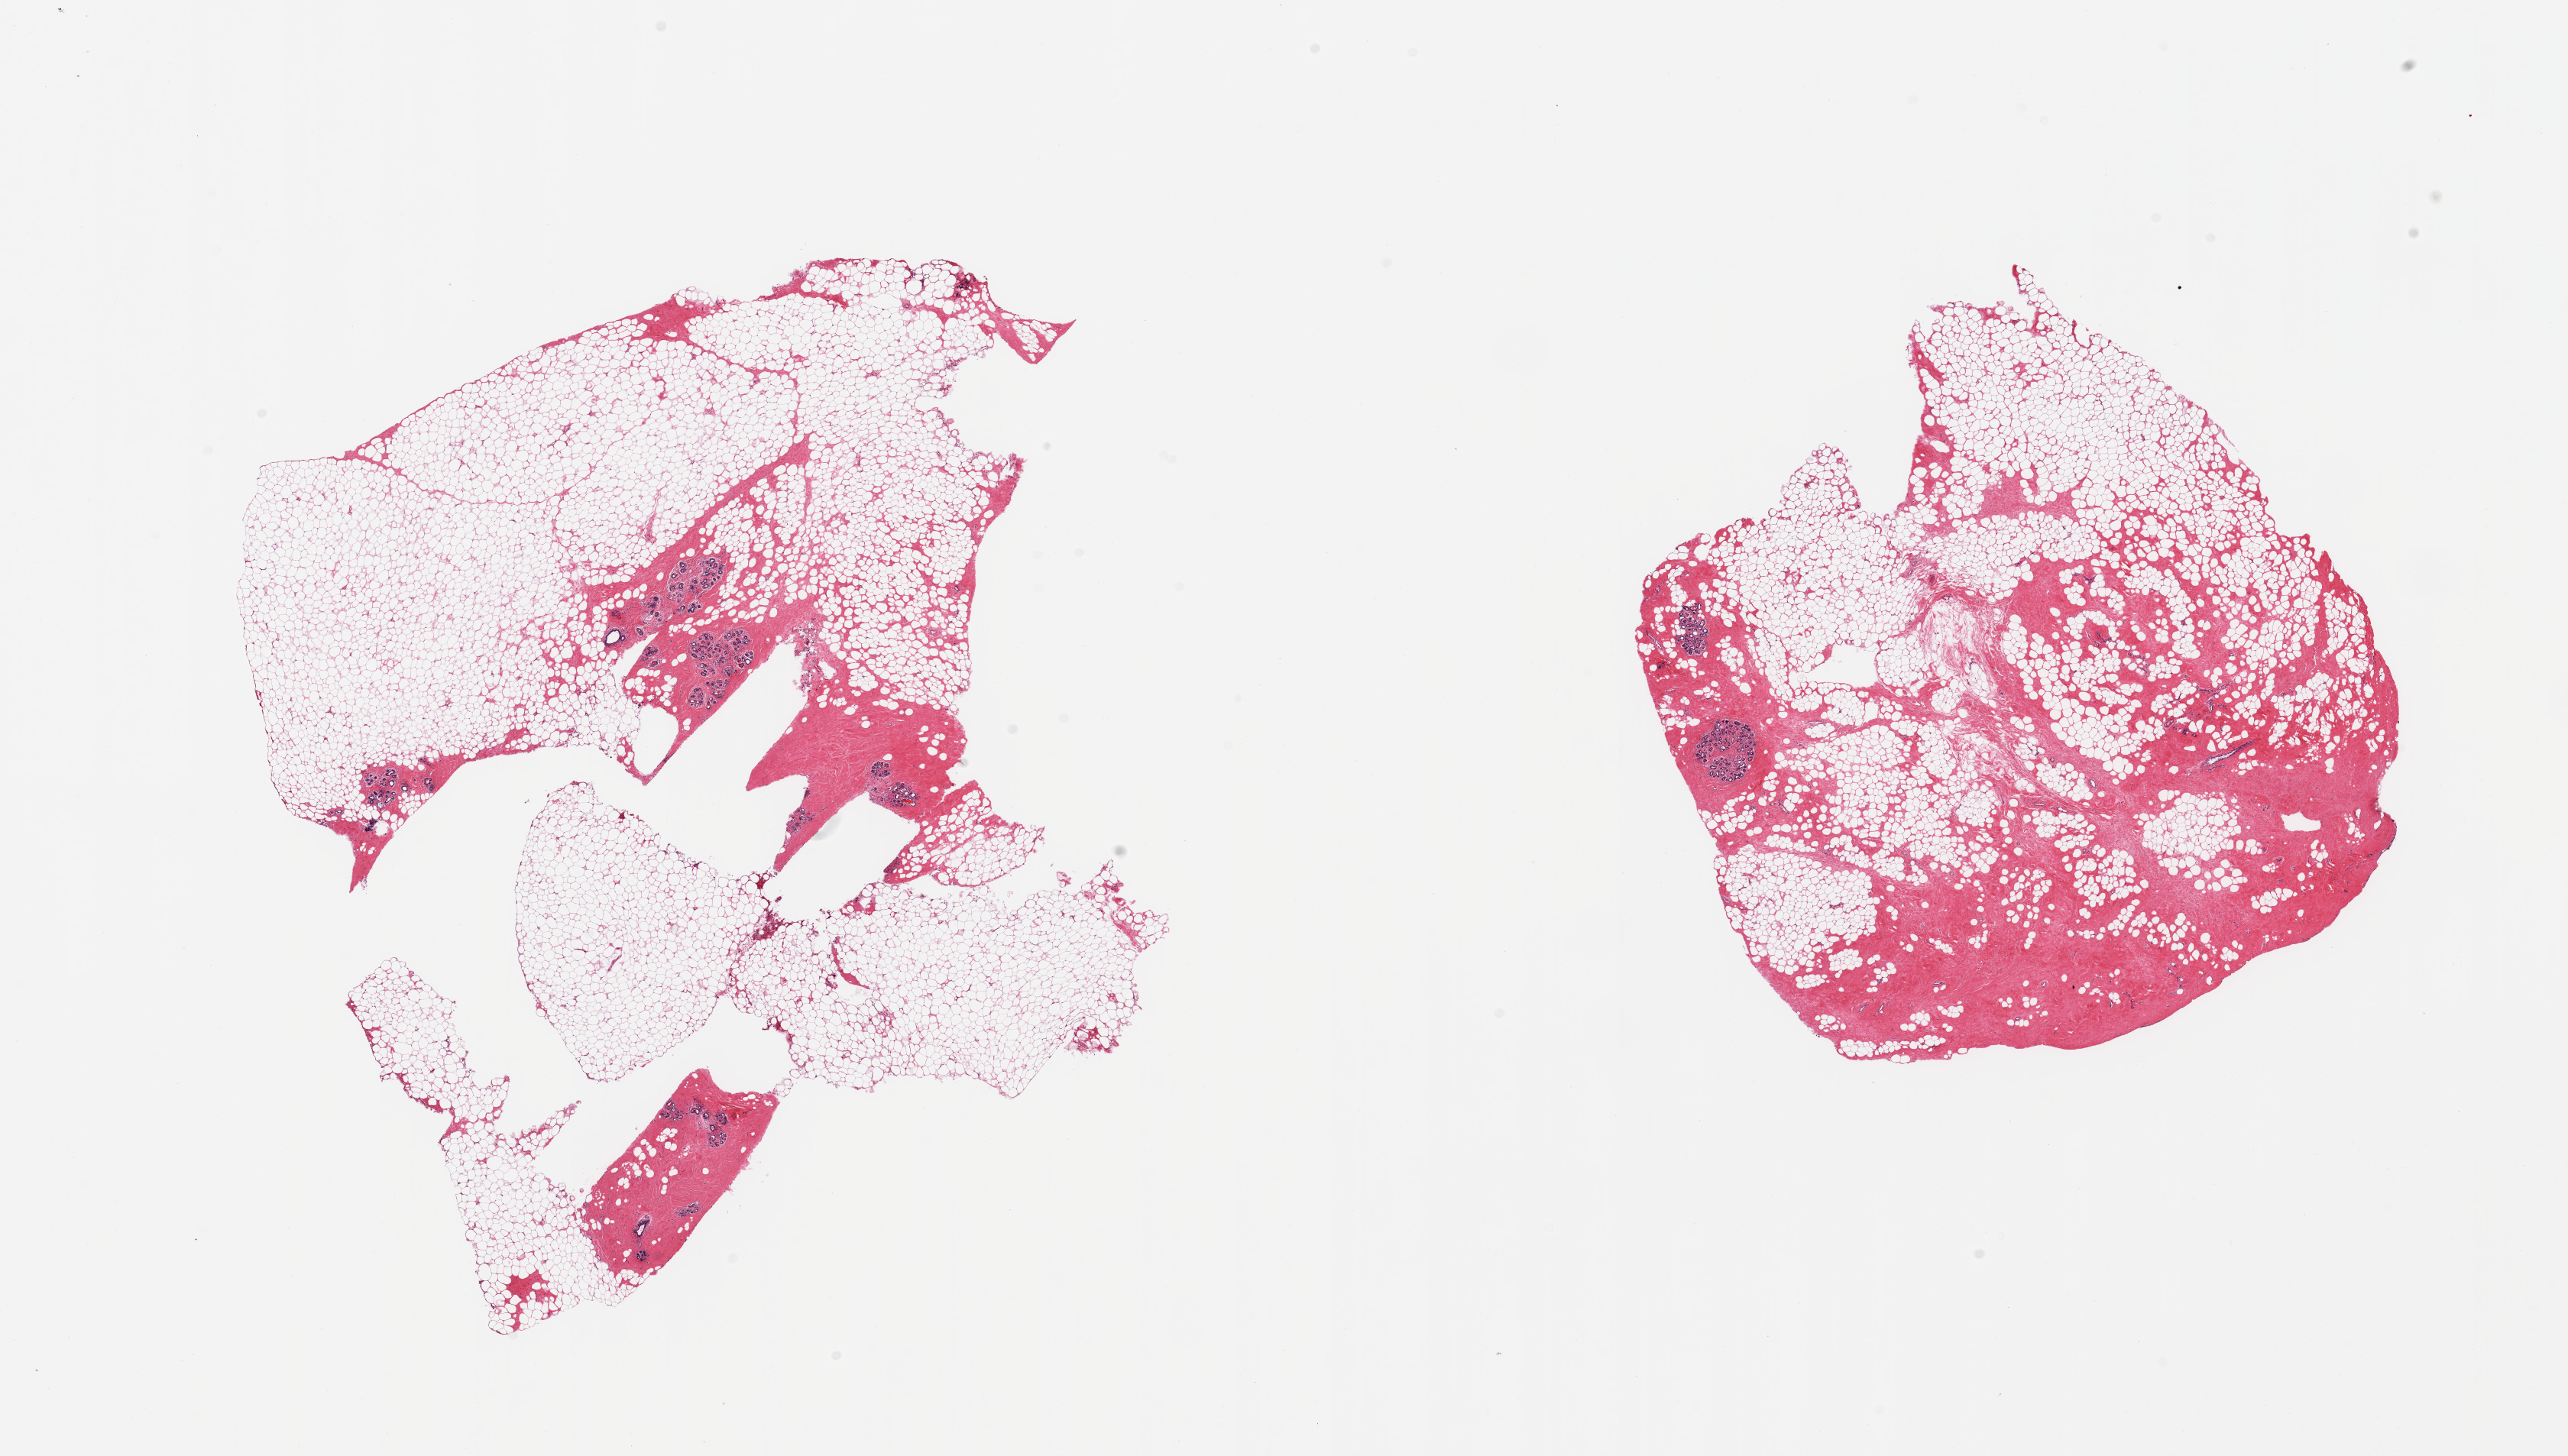
Whole-slide image, hematoxylin and eosin (H&E) stain, whole scanned area (about 26.6 x 15.1 mm, acquisition: 20x scan) shown as a low-resolution overview. PAXgene-fixed, paraffin-embedded tissue. Sampled site (target tissue): breast. Donor tissue sample. Donor: male.
Review note (as recorded): 2 pieces; fibroadipose tissue with mammary ducts.